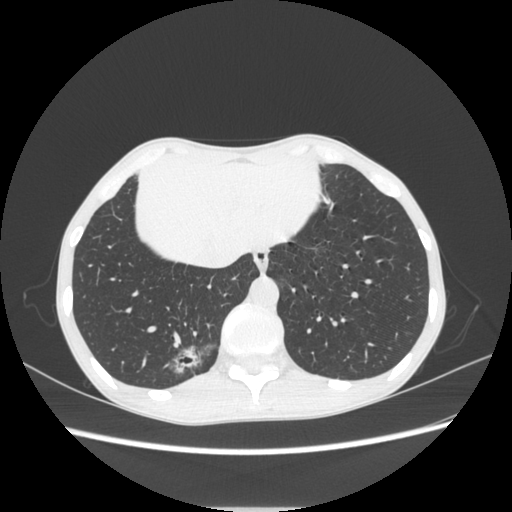
Chest CT, one axial slice. Slice 66 of 272 in the series (ordered by position). Reconstruction kernel STANDARD. Lung window (W 1500 / L -600 HU). 512 × 512 image matrix. Patient: female, 51 years. From the clinical record (not read from this slice): clinical TNM (as recorded): T1c N0 M0.
Structures marked on this image (rectangle marked by the reading radiologist):
- lung tumour (recorded histology: adenocarcinoma): bounding box [x1, y1, x2, y2] px = [165, 339, 220, 387]